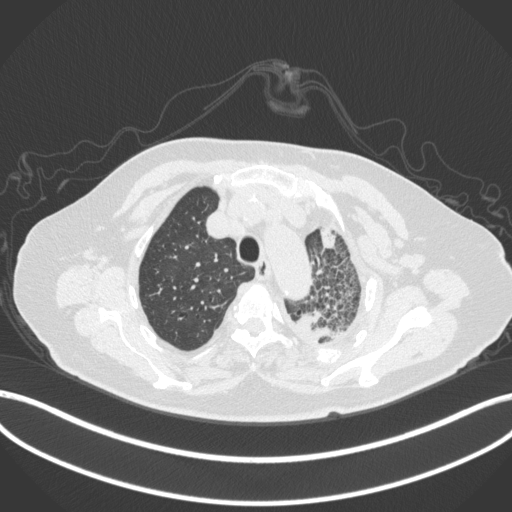
Chest CT, one axial slice; position 317 of 399 along the scan axis; reconstruction kernel B31f; lung window (W 1500 / L -600 HU); 1 mm slice thickness; 512 × 512 image matrix, field of view 400 × 400 mm. Patient: female, 75 years. Case-level facts recorded for this patient, not image findings: clinical TNM (as recorded): T3 N3 M1.
Structures marked on this image (bounding box drawn by a radiologist):
- lung tumour (recorded histology: adenocarcinoma): bounding box (x1, y1, x2, y2) in pixels: (294, 304, 343, 351)